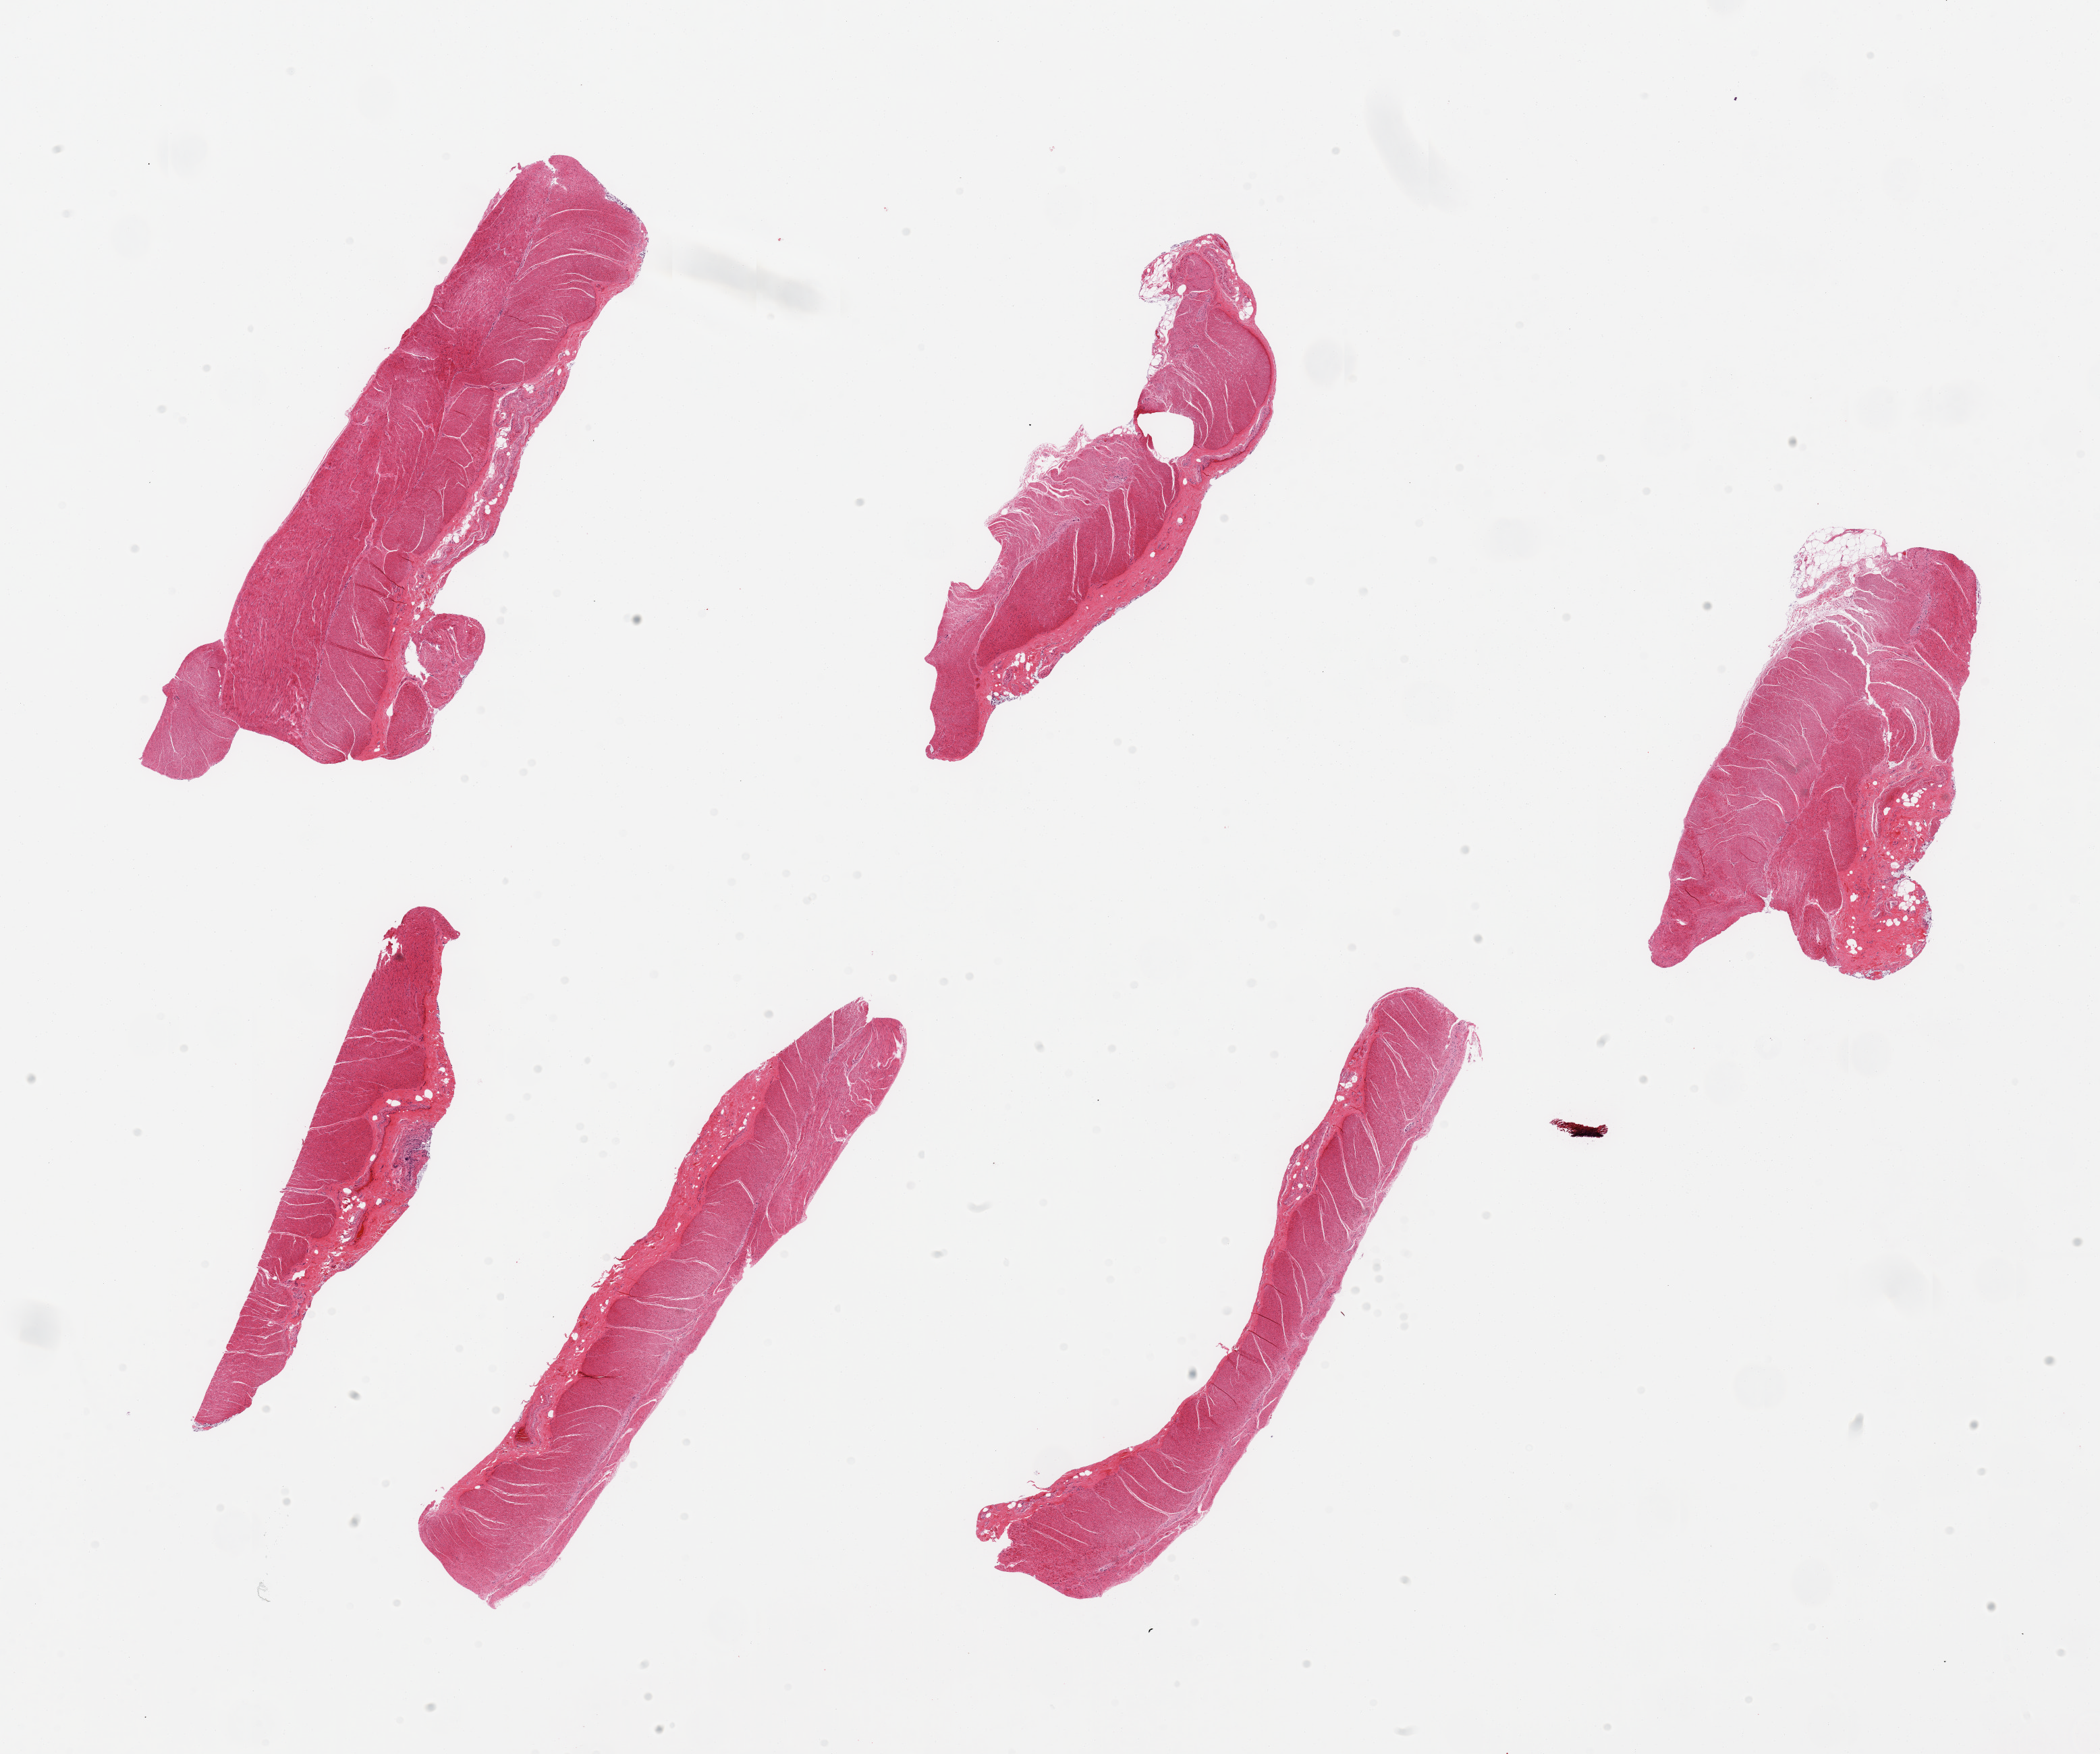
Digitized haematoxylin and eosin-stained section, brightfield — a low-resolution overview of the entire scanned area, about 24.6 x 20.6 mm. PAXgene-fixed, paraffin-embedded tissue. Section of sigmoid colon (target tissue). Tissue donor sample. Donor: male.
Reviewer comment on this tissue sample: 6 pieces, predominantly muscularis with small attachment of fat and residual autolyzed mucosa.